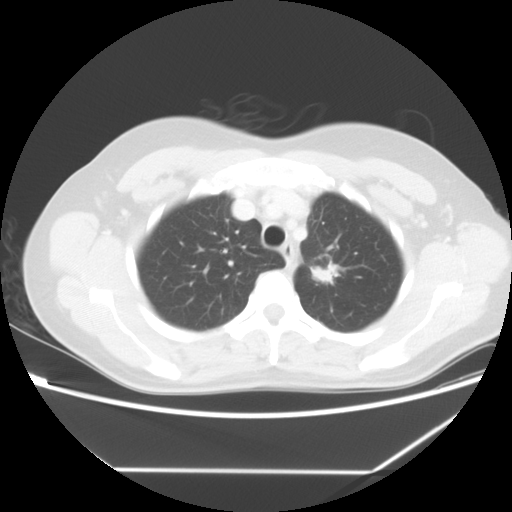
Chest CT, one axial slice. Slice 47 of 60 in the series (ordered by position). Lung window (W 1500 / L -600 HU). 5 mm slice thickness. 512 × 512 image matrix, field of view 367 × 367 mm. Female patient, age 43 years. Case-level facts recorded for this patient, not image findings: clinical TNM (as recorded): T1c N0 M1b.
Outlined on this slice (bounding box drawn by a radiologist):
- lung tumour (recorded histology: adenocarcinoma): bounding box (x1, y1, x2, y2) in pixels: (306, 259, 345, 285)